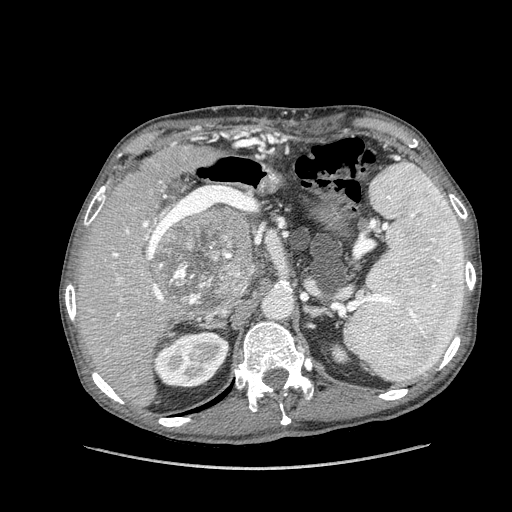
Contrast-enhanced abdominal CT (liver protocol), one axial slice; position 85 of 162 along the scan axis; reconstruction kernel STANDARD; 100 kVp; soft-tissue window (W 400 / L 40 HU); 2.5 mm slice thickness; 512 × 512 image matrix, field of view 400 × 400 mm. From the clinical record (not read from this slice): diagnosis: hepatocellular carcinoma (patient treated with transarterial chemoembolisation; whether this scan precedes or follows treatment is not stated here); TNM stage (as recorded): Stage-IIIA.
Annotated regions visible in this slice (semi-automatic segmentation, software-assisted and operator-edited):
- liver parenchyma outside the tumour (the mass and vessels are separate outlines, so this box may not span the whole liver): bounding box (x1, y1, x2, y2) in pixels: (76, 142, 256, 406)
- mass: (153, 205, 256, 310)
- liver vessels: (95, 143, 183, 317)